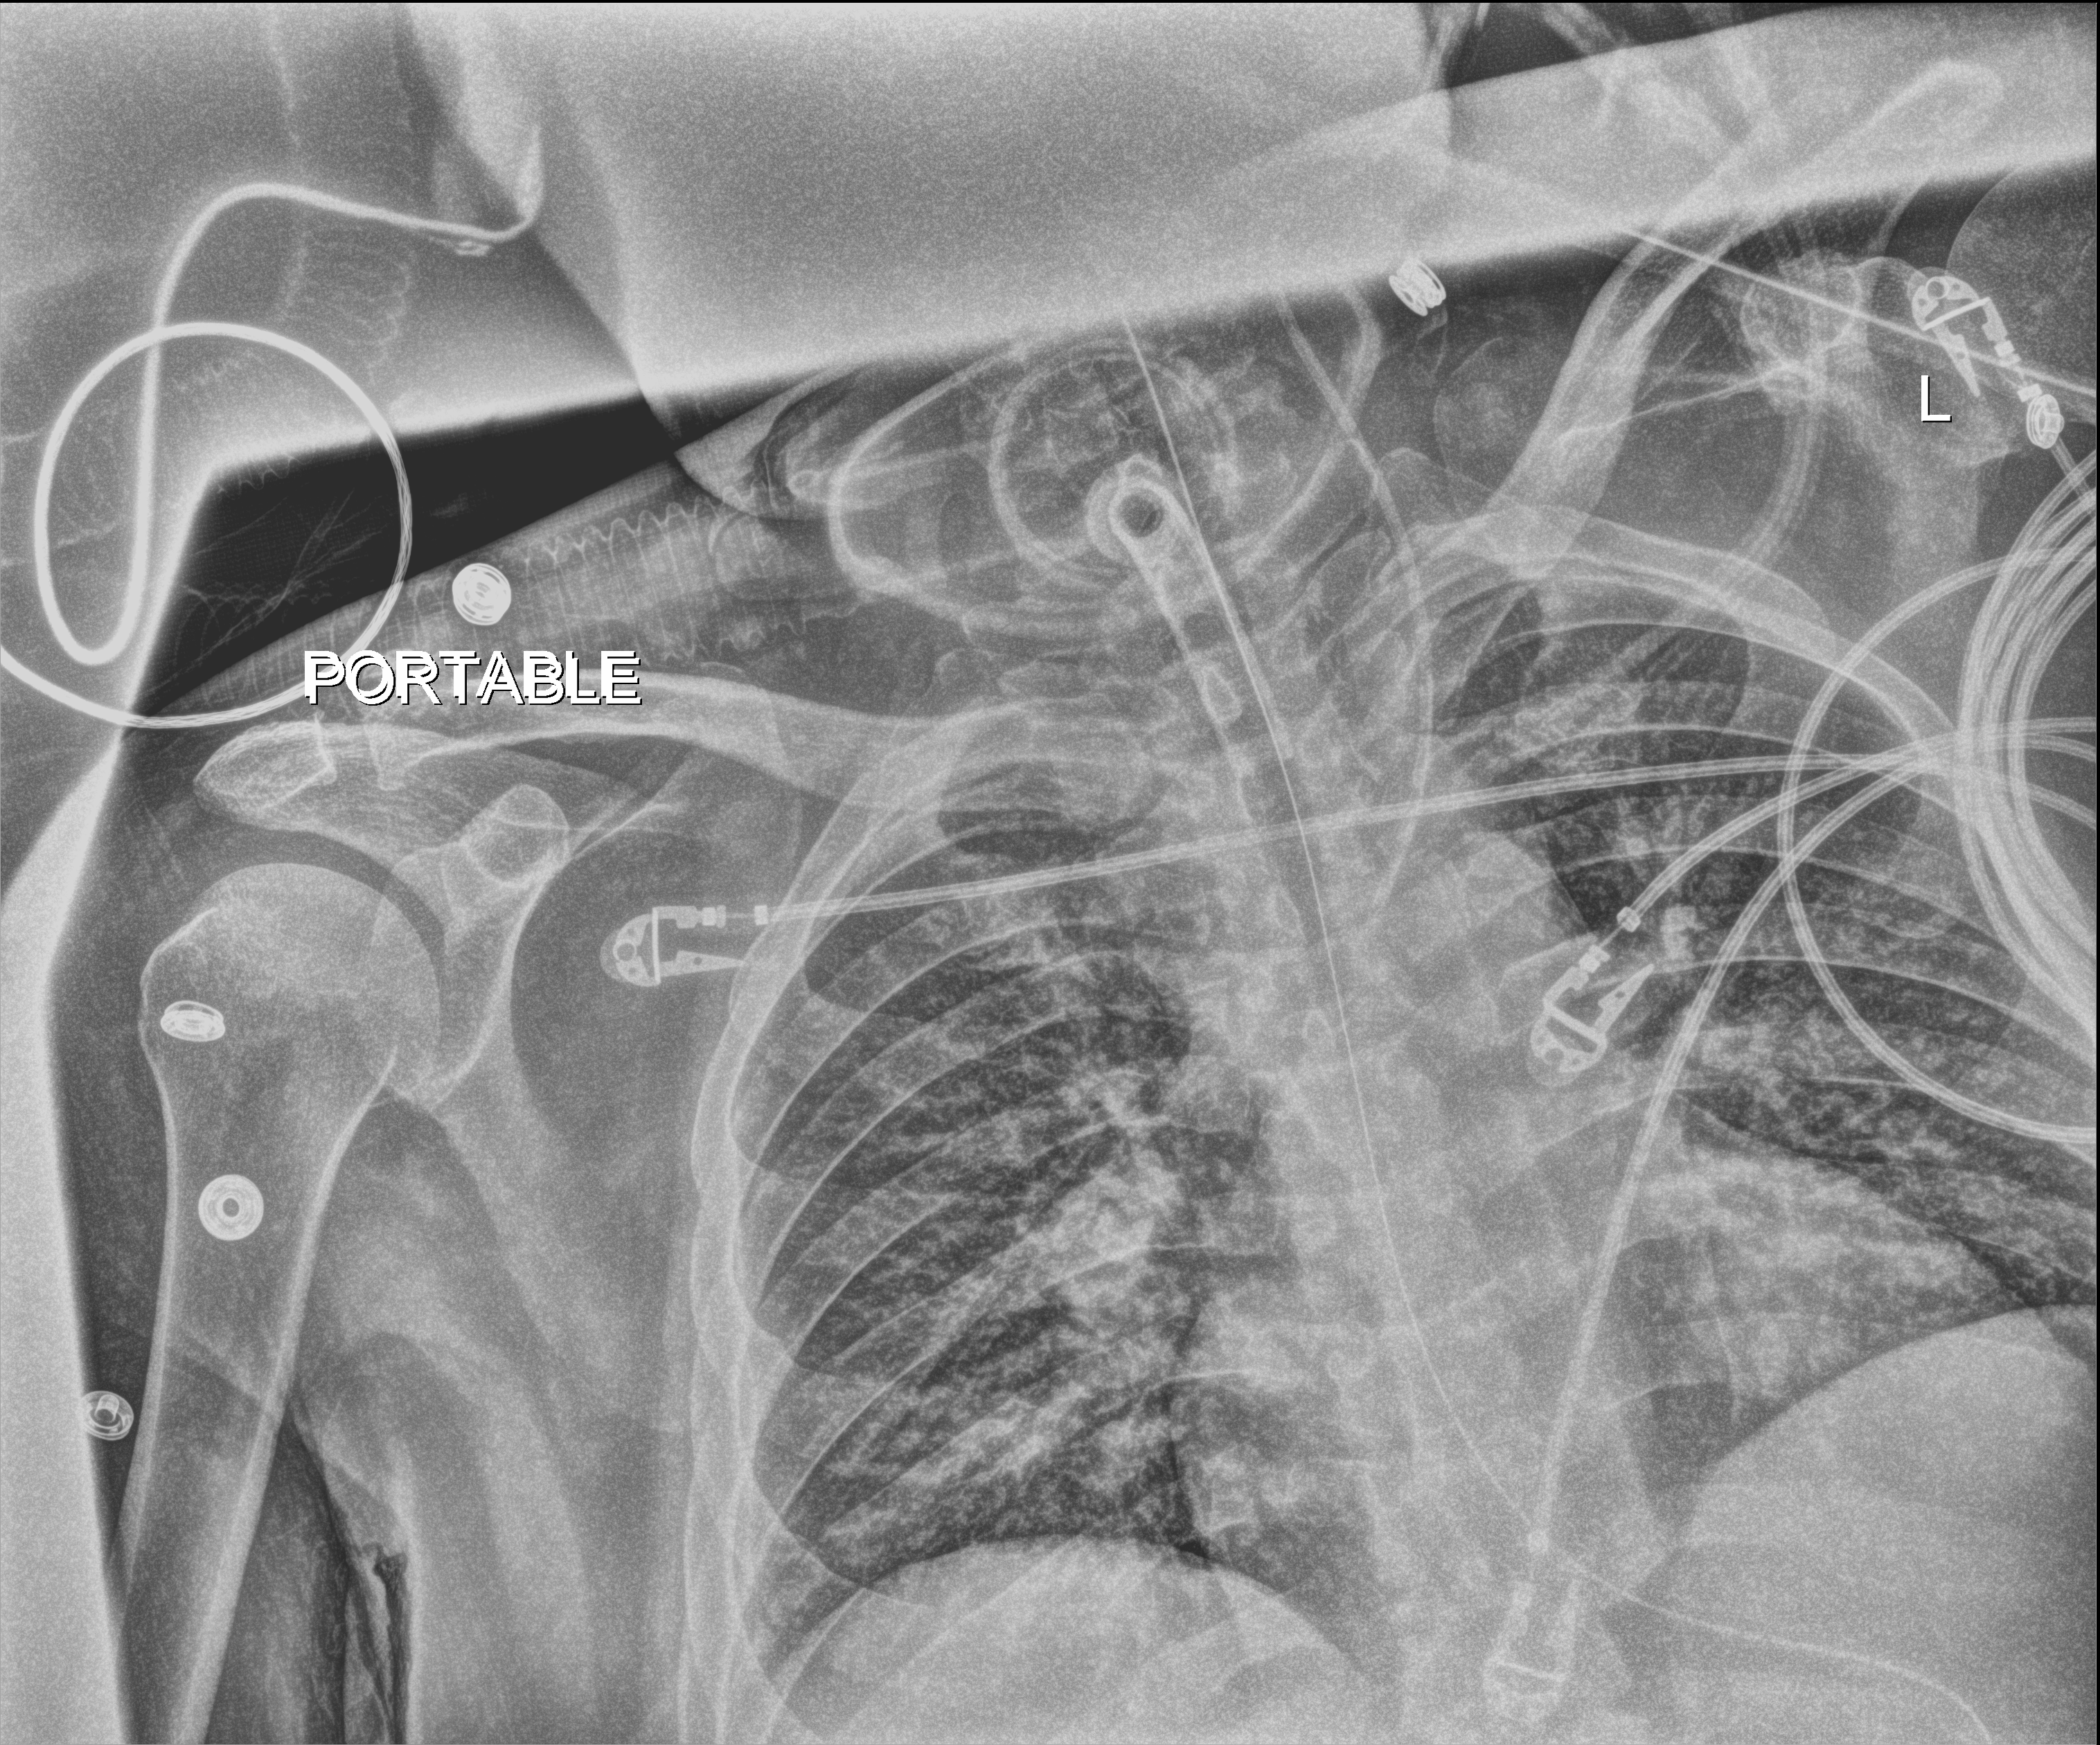
Chest X-ray (portable); anteroposterior (AP) projection. Female patient hospitalised with COVID-19, age 75–90 years.
From the hospital-stay record, not from the radiograph (when in the stay this image was taken is not recorded): smoking status (admission record): former; admitted to intensive care during this hospital stay: yes; mechanically ventilated during this hospital stay: yes.